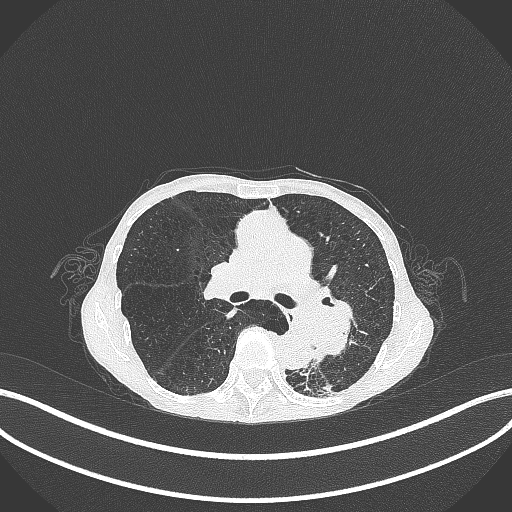
Chest CT, one axial slice. Position 165 of 347 along the scan axis. Reconstruction kernel B70f. Lung window (W 1500 / L -600 HU). 512 × 512 image matrix. Patient: female, 70 years. Case-level facts recorded for this patient, not image findings: clinical TNM (as recorded): T3 N0 M0; histopathological grade: G3.
Annotated regions visible in this slice (bounding box drawn by a radiologist):
- lung tumour (recorded histology: small cell carcinoma): bounding box [x1, y1, x2, y2] px = [288, 302, 368, 362]